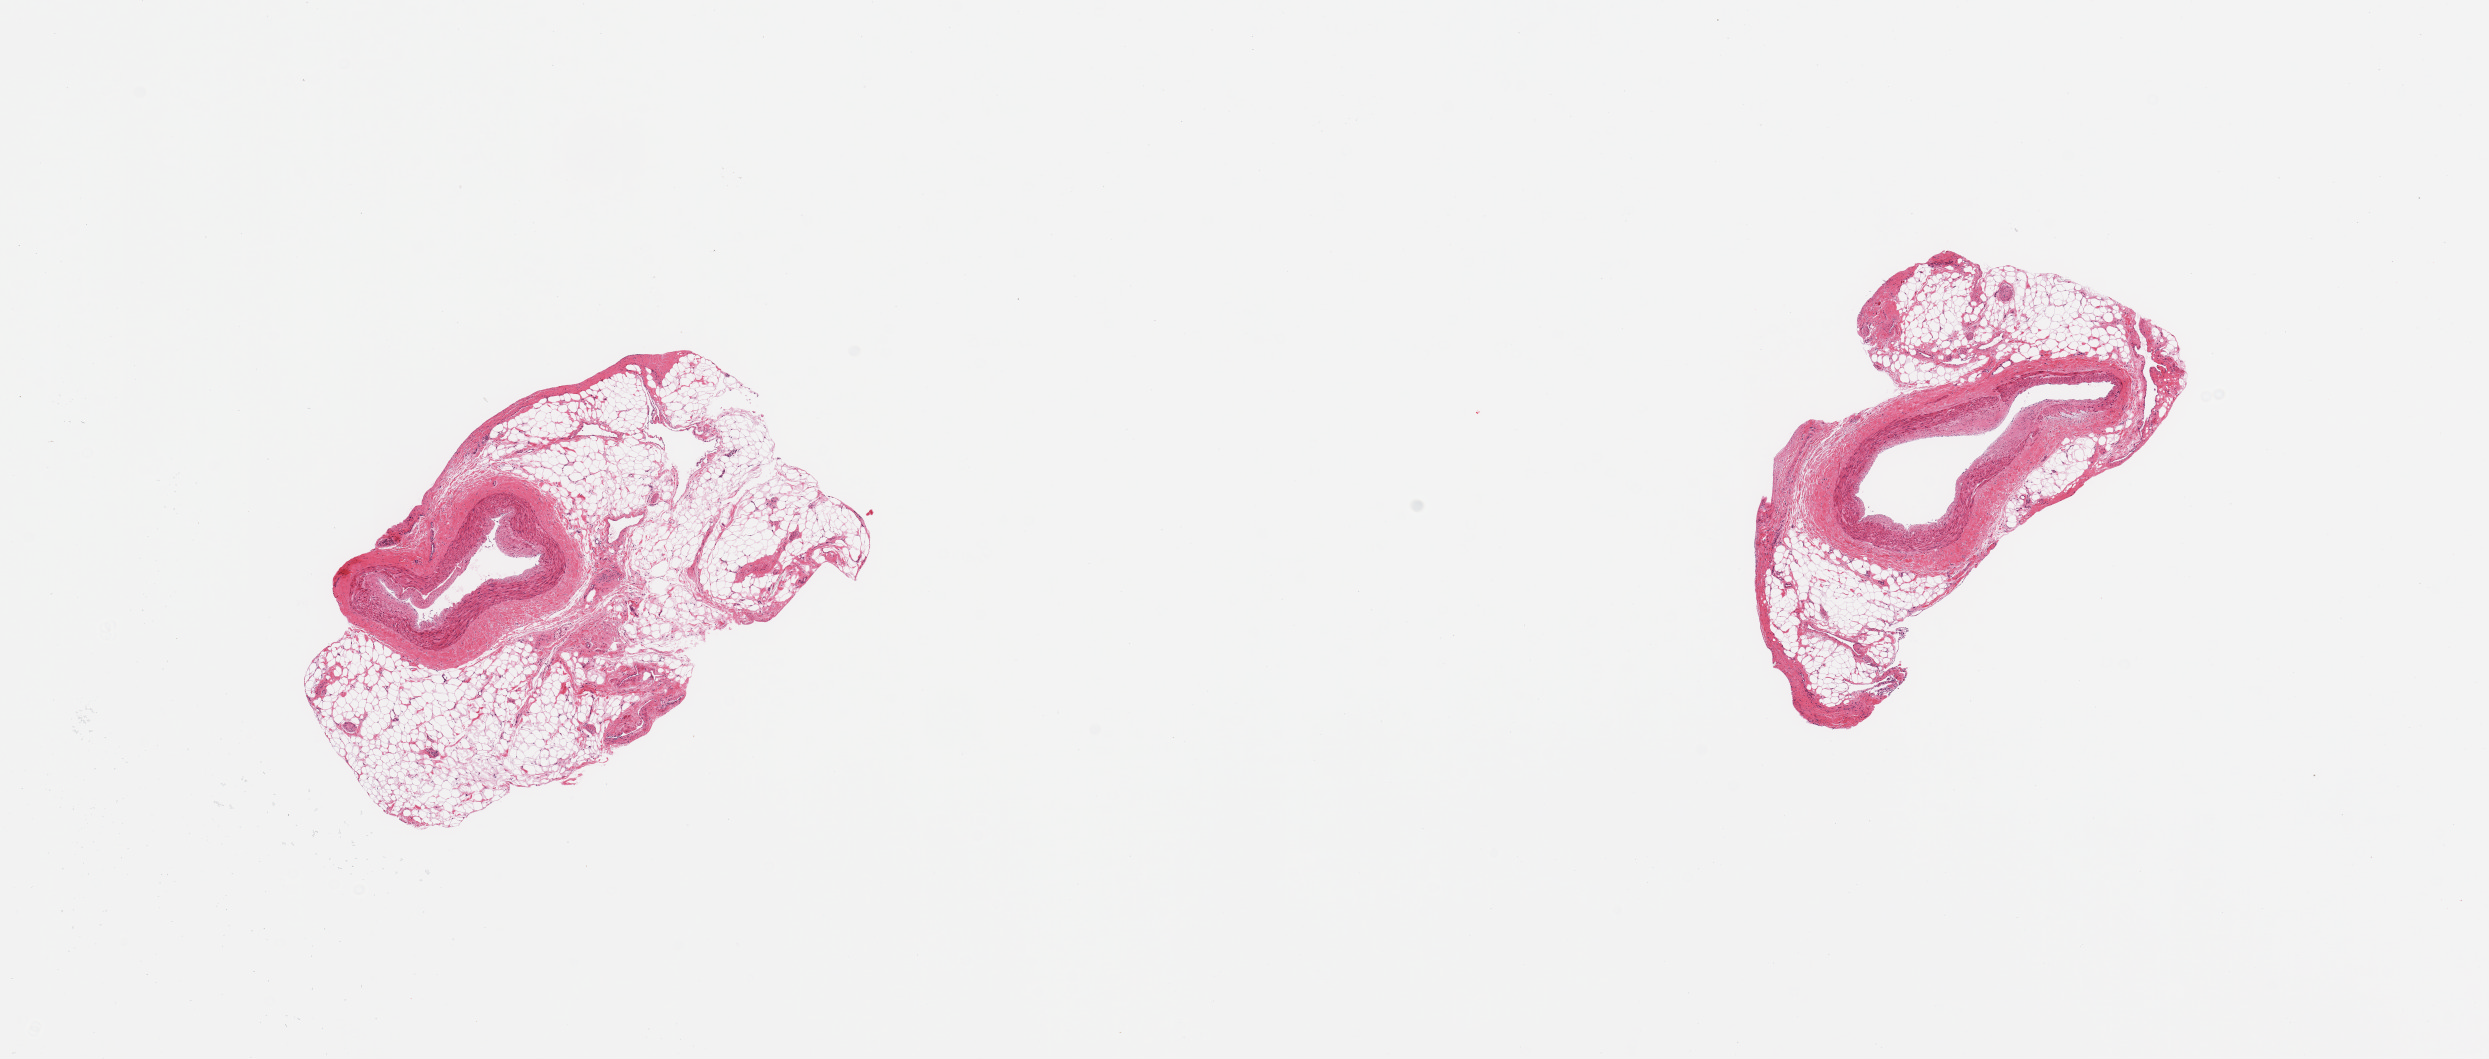
Whole-slide image, hematoxylin and eosin (H&E) stain, whole scanned area (about 19.7 x 8.4 mm, from a 20x scan) shown as a low-resolution overview, PAXgene-fixed, paraffin-embedded tissue, target tissue: coronary artery, donor tissue sample. Female donor.
Reviewer comment on this tissue sample: 2 pieces, probalbe branch twigs, >60% of tissue is epicardial fat; insufficient target artery.